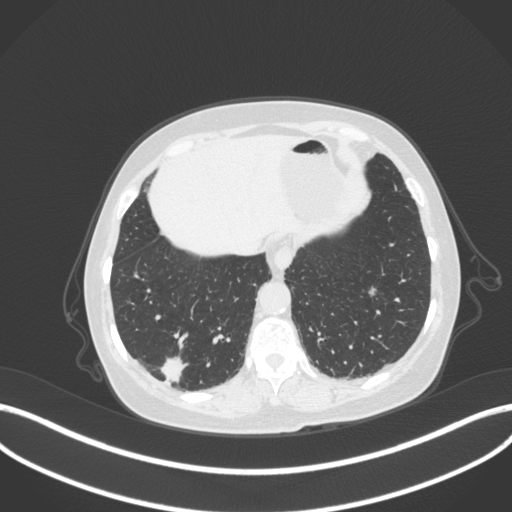
Chest CT, one axial slice; position 61 of 340 along the scan axis; reconstruction kernel B31f; 120 kVp; lung window (W 1500 / L -600 HU); 512 × 512 image matrix, field of view 400 × 400 mm. Female patient, age 69 years. Case-level facts recorded for this patient, not image findings: clinical TNM (as recorded): T1b N0 M0.
Outlined on this slice (rectangle marked by the reading radiologist):
- lung tumour (recorded histology: adenocarcinoma): bounding box (x1, y1, x2, y2) in pixels: (158, 350, 190, 385)